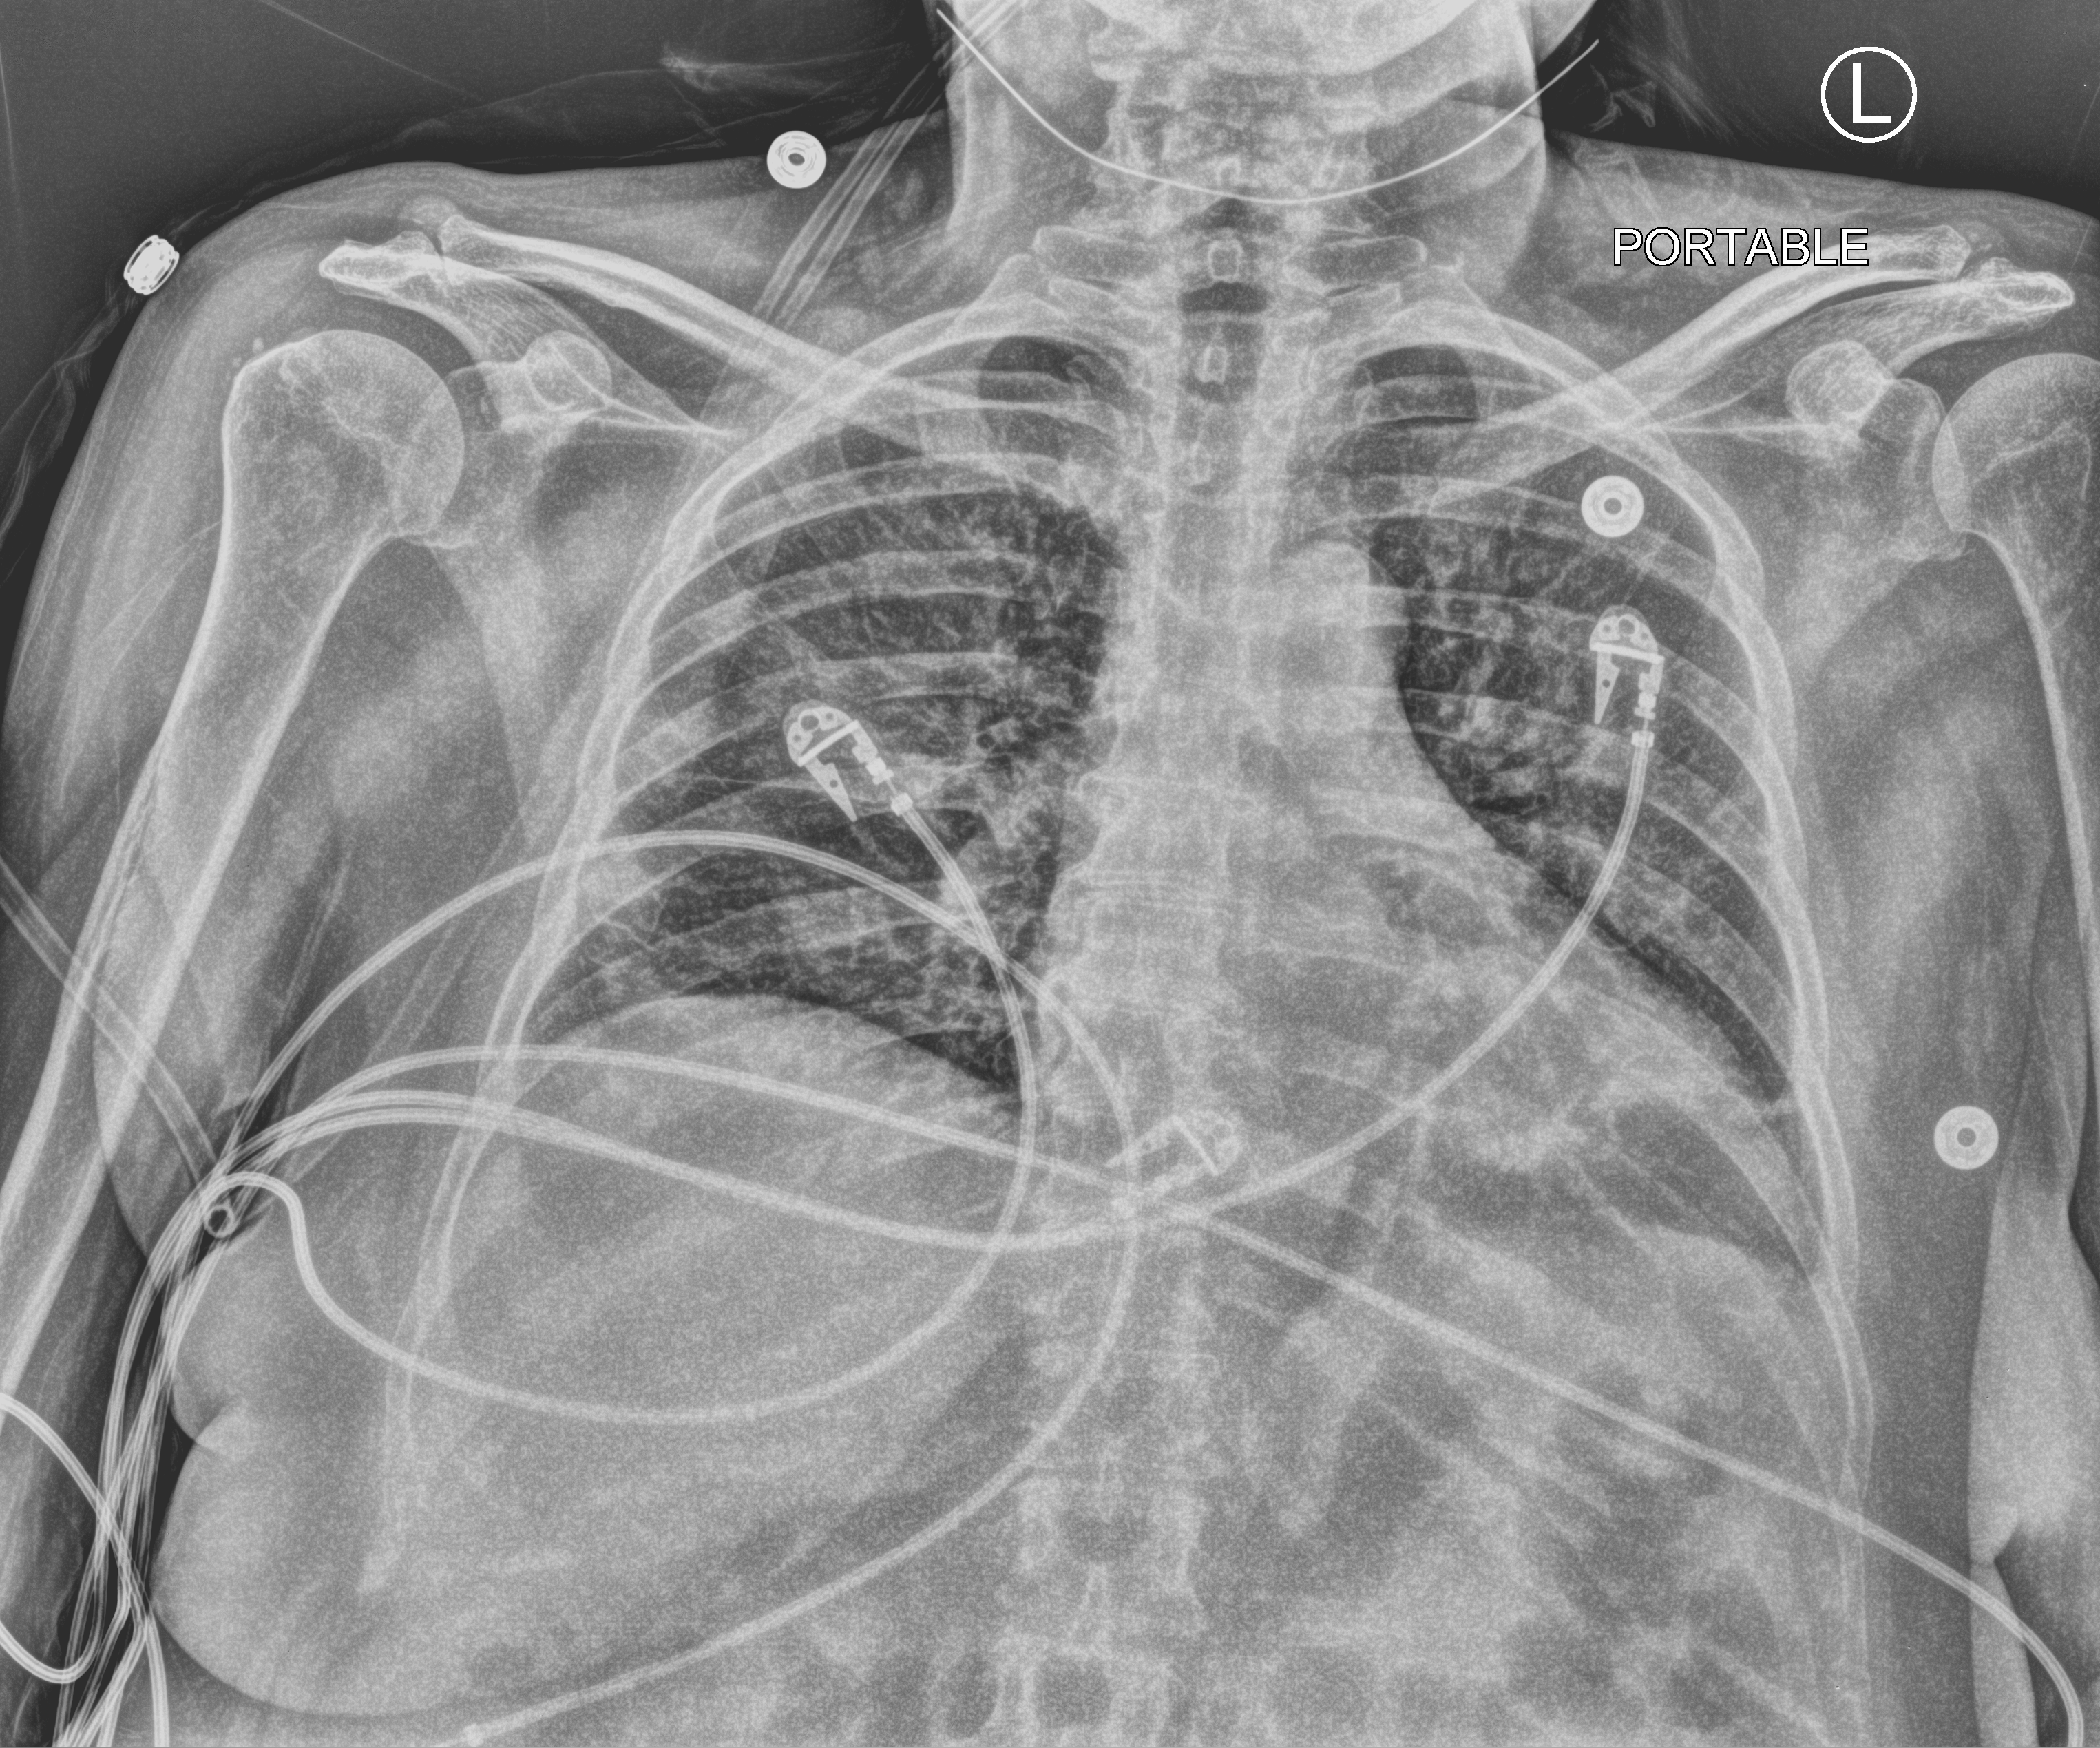
Portable chest radiograph, anteroposterior (AP) projection. Female patient hospitalised with COVID-19, age 60–74 years.
Hospital-stay facts (about this admission, not read from this image; timing relative to this image not recorded): hypertension (admission record): no.